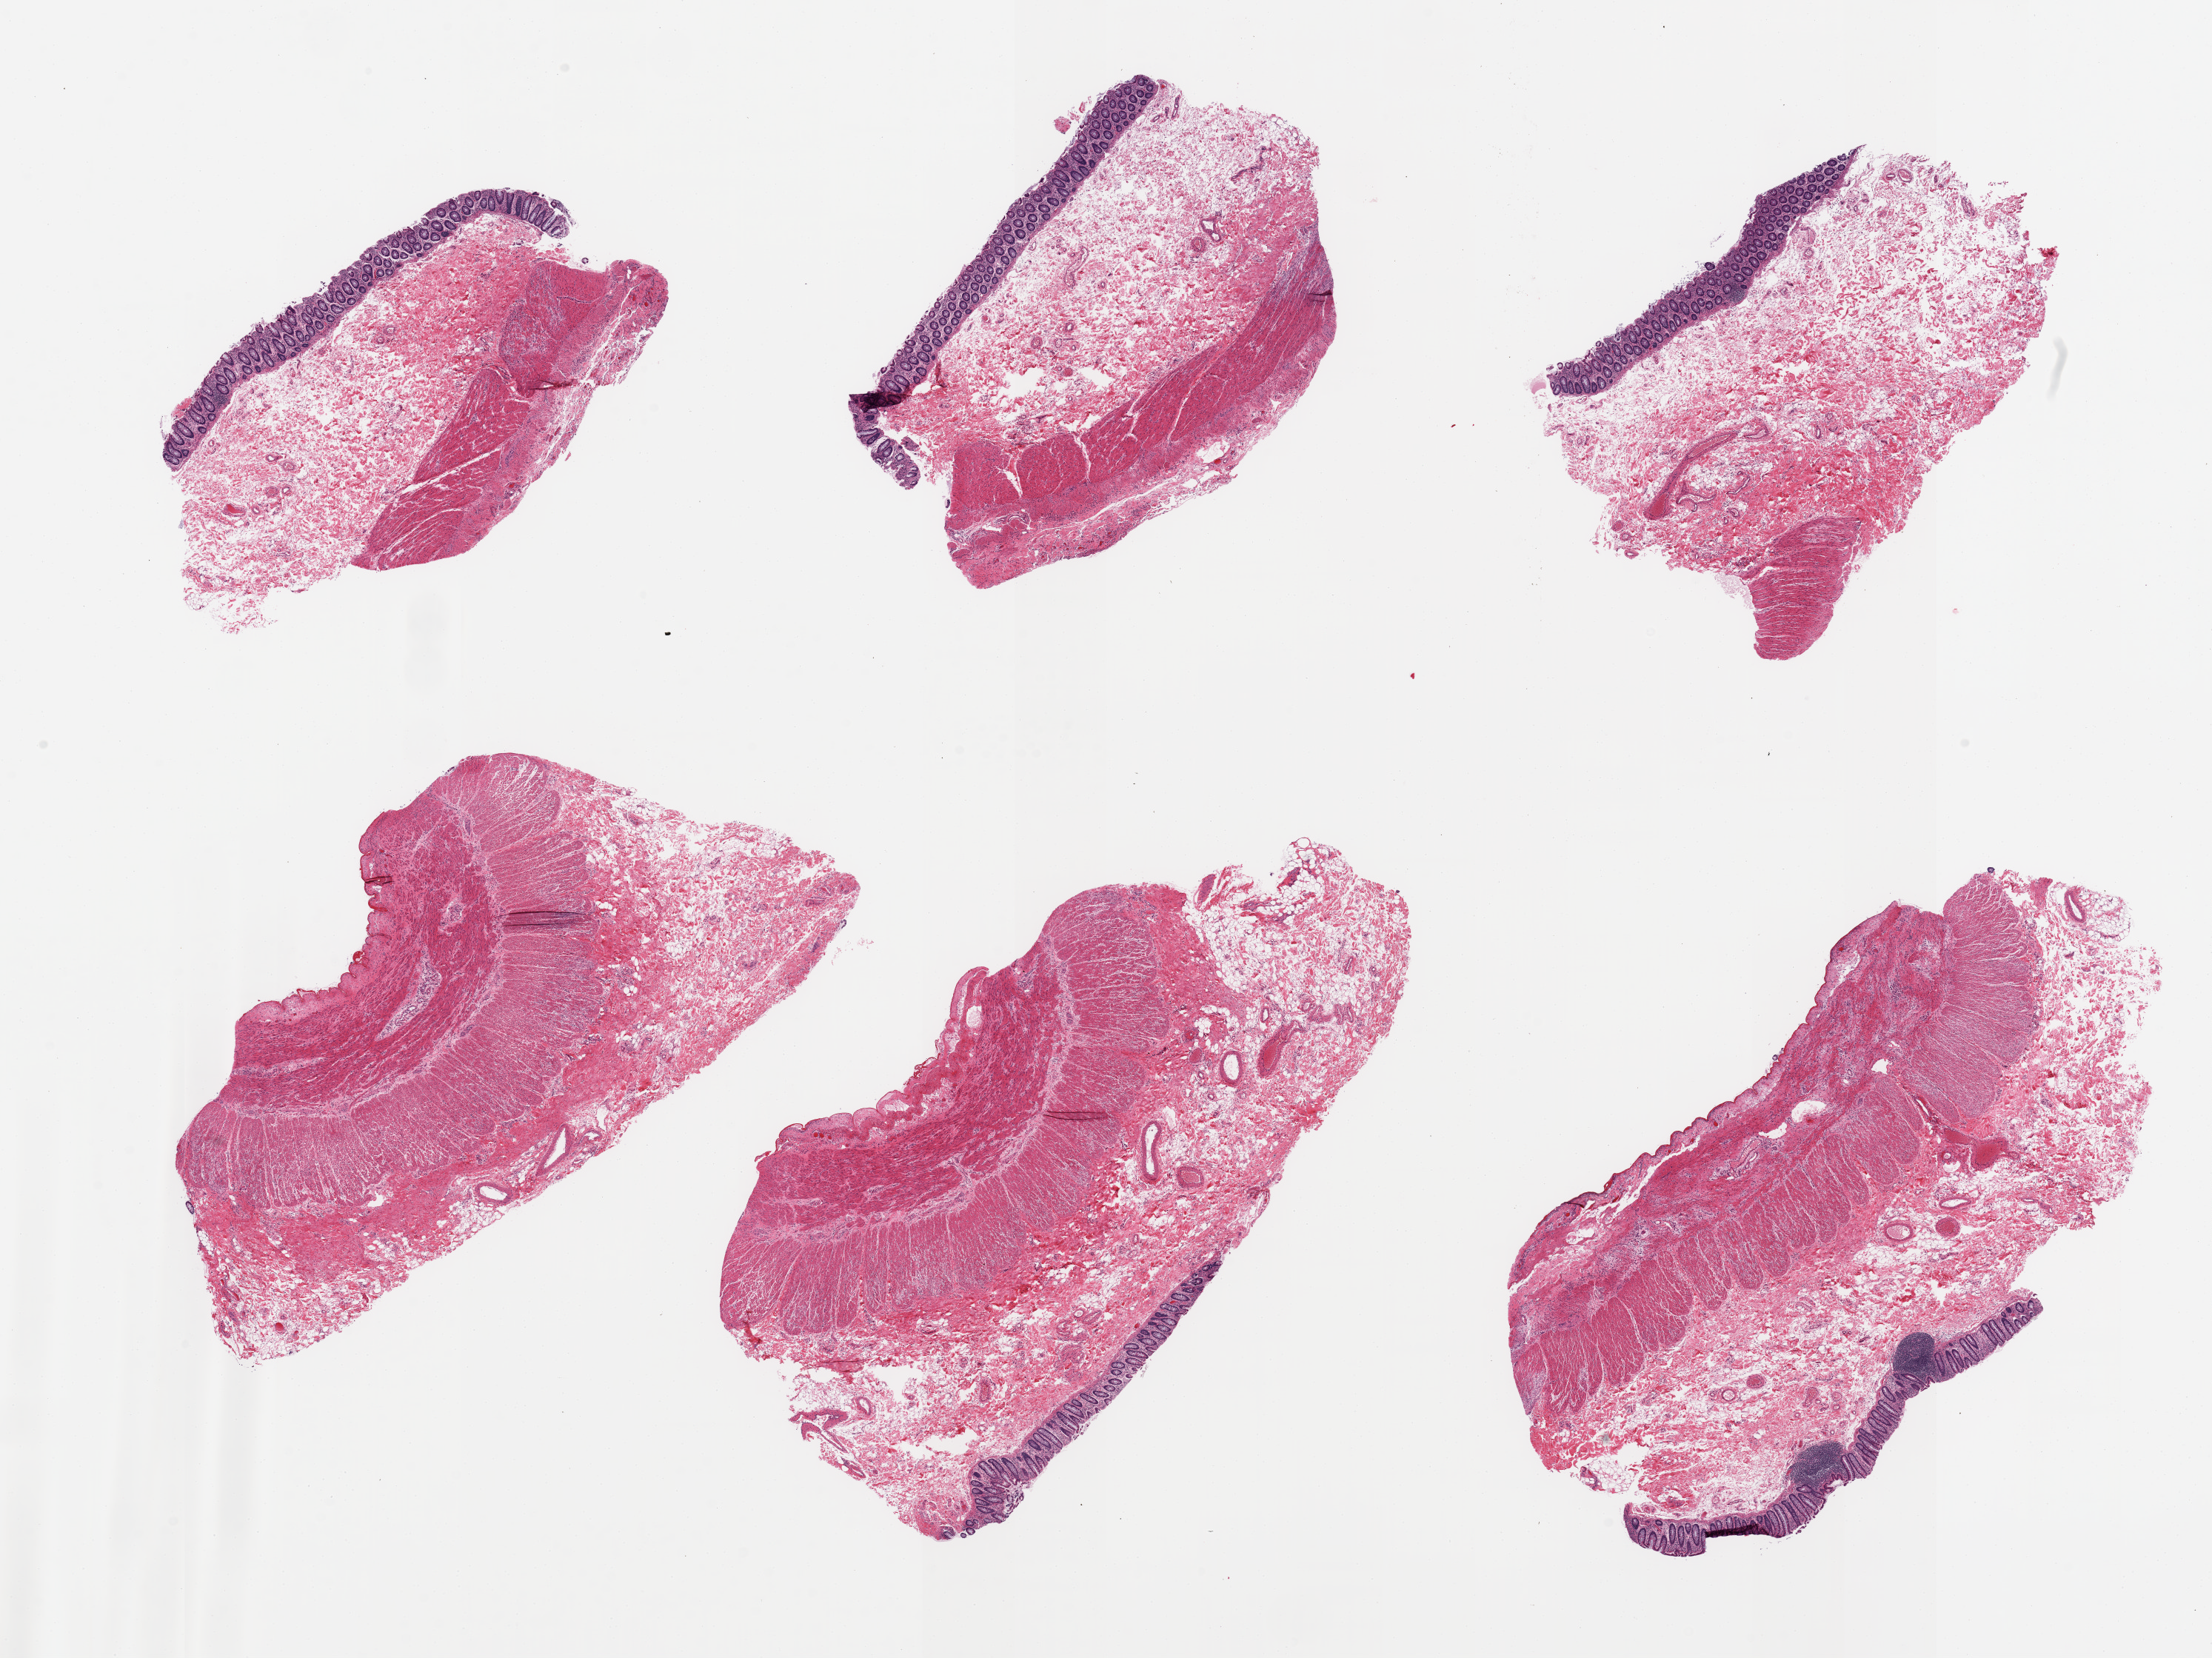
Haematoxylin and eosin whole-slide image — low-resolution overview of the scanned area, about 23.6 x 17.7 mm; PAXgene-fixed paraffin-embedded (PFPE) section; sampled site (target tissue): transverse colon; donor tissue sample. Male donor.
* reviewer comment on this tissue sample: 6 pieces, target mucosa up to ~0.4mm, ~10% thickness